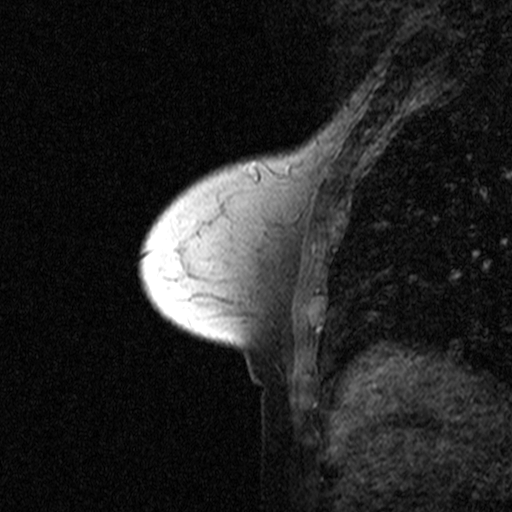
Breast MRI (dynamic contrast-enhanced), one sagittal slice. Position 15 of 44 along the scan axis. Dynamic contrast-enhanced study with each time point stored as its own series, time point 2 of 3 at this slice position (early post-contrast, ordered by acquisition time). 1.5 T. TE 4.5 ms, TR 11 ms. 3 mm slice thickness. 512 × 512 image matrix, field of view 200 × 200 mm. Female patient, age 53 years. Case-level facts recorded for this patient, not image findings: setting: breast cancer imaged before/during neoadjuvant chemotherapy; receptor status: HR-positive, HER2-negative.
Structures marked on this image (semi-automatically segmented with operator editing):
- analysis volume of interest (the breast-tissue region the enhancement analysis was run in; not a lesion): box from (x=170, y=153) to (x=277, y=273) px
- tumour enhancement mask (voxels above the 90 % enhancement threshold inside the analysis volume of interest): (x=254, y=166)–(x=262, y=181)